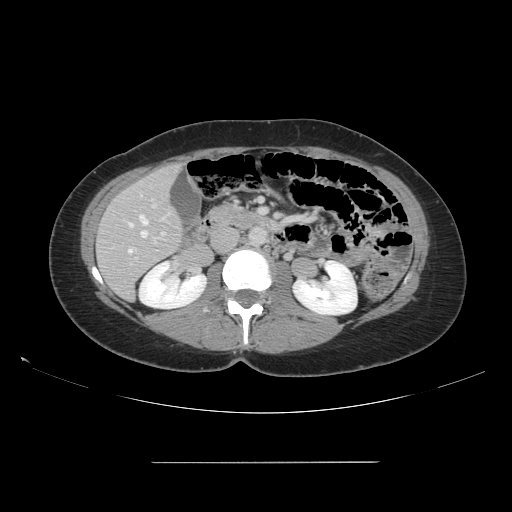
Contrast-enhanced abdominal CT, one axial slice; position 64 of 151 along the scan axis; intravenous contrast given; soft-tissue window (W 400 / L 40 HU); 2.5 mm slice thickness; 512 × 512 image matrix, field of view 421 × 421 mm. Female patient, age 46 years. From the clinical record (not read from this slice): diagnosis: colorectal cancer liver metastases, imaged before liver resection; multiple liver metastases: yes.
Outlined on this slice (manually delineated by an expert):
- hepatic veins: bounding box (x1, y1, x2, y2) in pixels: (128, 215, 149, 254)
- liver: (98, 166, 183, 299)
- planned liver remnant (the part of the liver to remain after resection): (98, 165, 183, 299)
- portal vein (with intrahepatic branches): (135, 199, 165, 260)